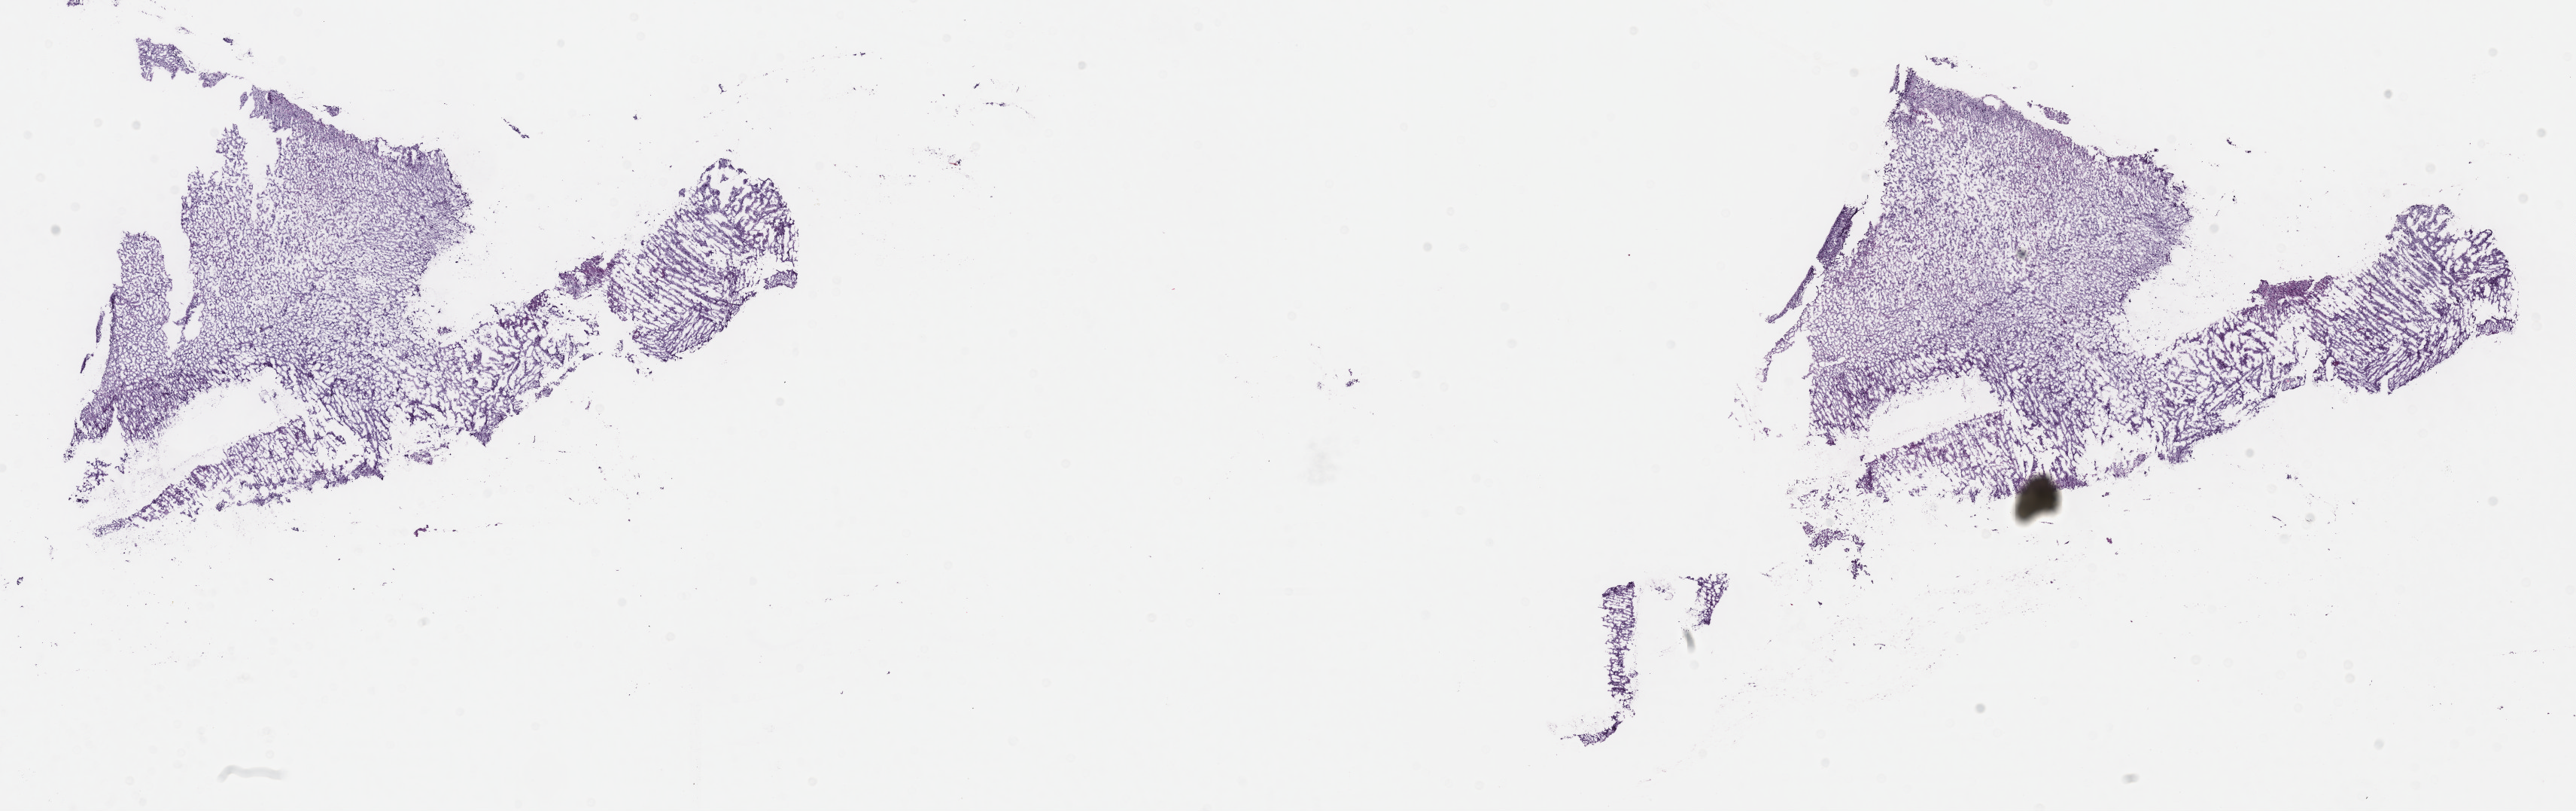
Digitized H&E-stained tissue section (whole slide), shown as a low-resolution overview of the whole scanned area (about 27.7 x 8.7 mm, from a 40x scan), frozen section, primary tumour sample from the brain. Male patient; age at initial diagnosis 20 years. Histologic grade: G2 (moderately differentiated). Slide review estimates, as recorded: tumour cells 30%, tumour nuclei 80%, normal cells 10%, stromal cells 60%, necrosis 0%. Inflammatory infiltration, as recorded: lymphocyte infiltration 0%, monocyte infiltration 0%, neutrophil infiltration 0%.
• histologic diagnosis: Astrocytoma, NOS (cerebrum)
• laterality: right